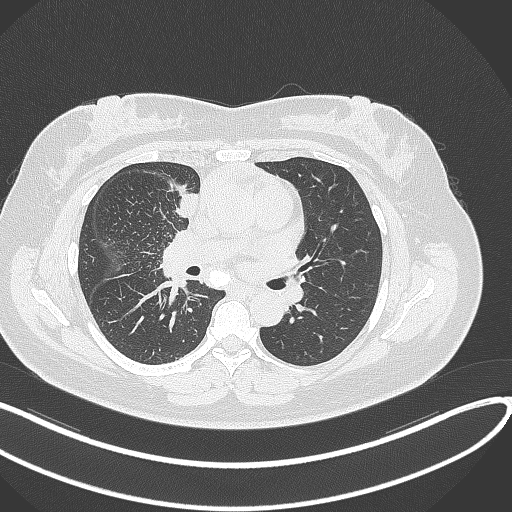
Chest CT, one axial slice. Position 146 of 303 along the scan axis. 120 kVp. Lung window (W 1500 / L -600 HU). 1 mm slice thickness. 512 × 512 image matrix, field of view 400 × 400 mm. Patient: female, 46 years. Case-level facts recorded for this patient, not image findings: clinical TNM (as recorded): T2a N1 M0.
Outlined on this slice (bounding box drawn by a radiologist):
- lung tumour (recorded histology: adenocarcinoma): bounding box (x1, y1, x2, y2) in pixels: (173, 189, 200, 223)